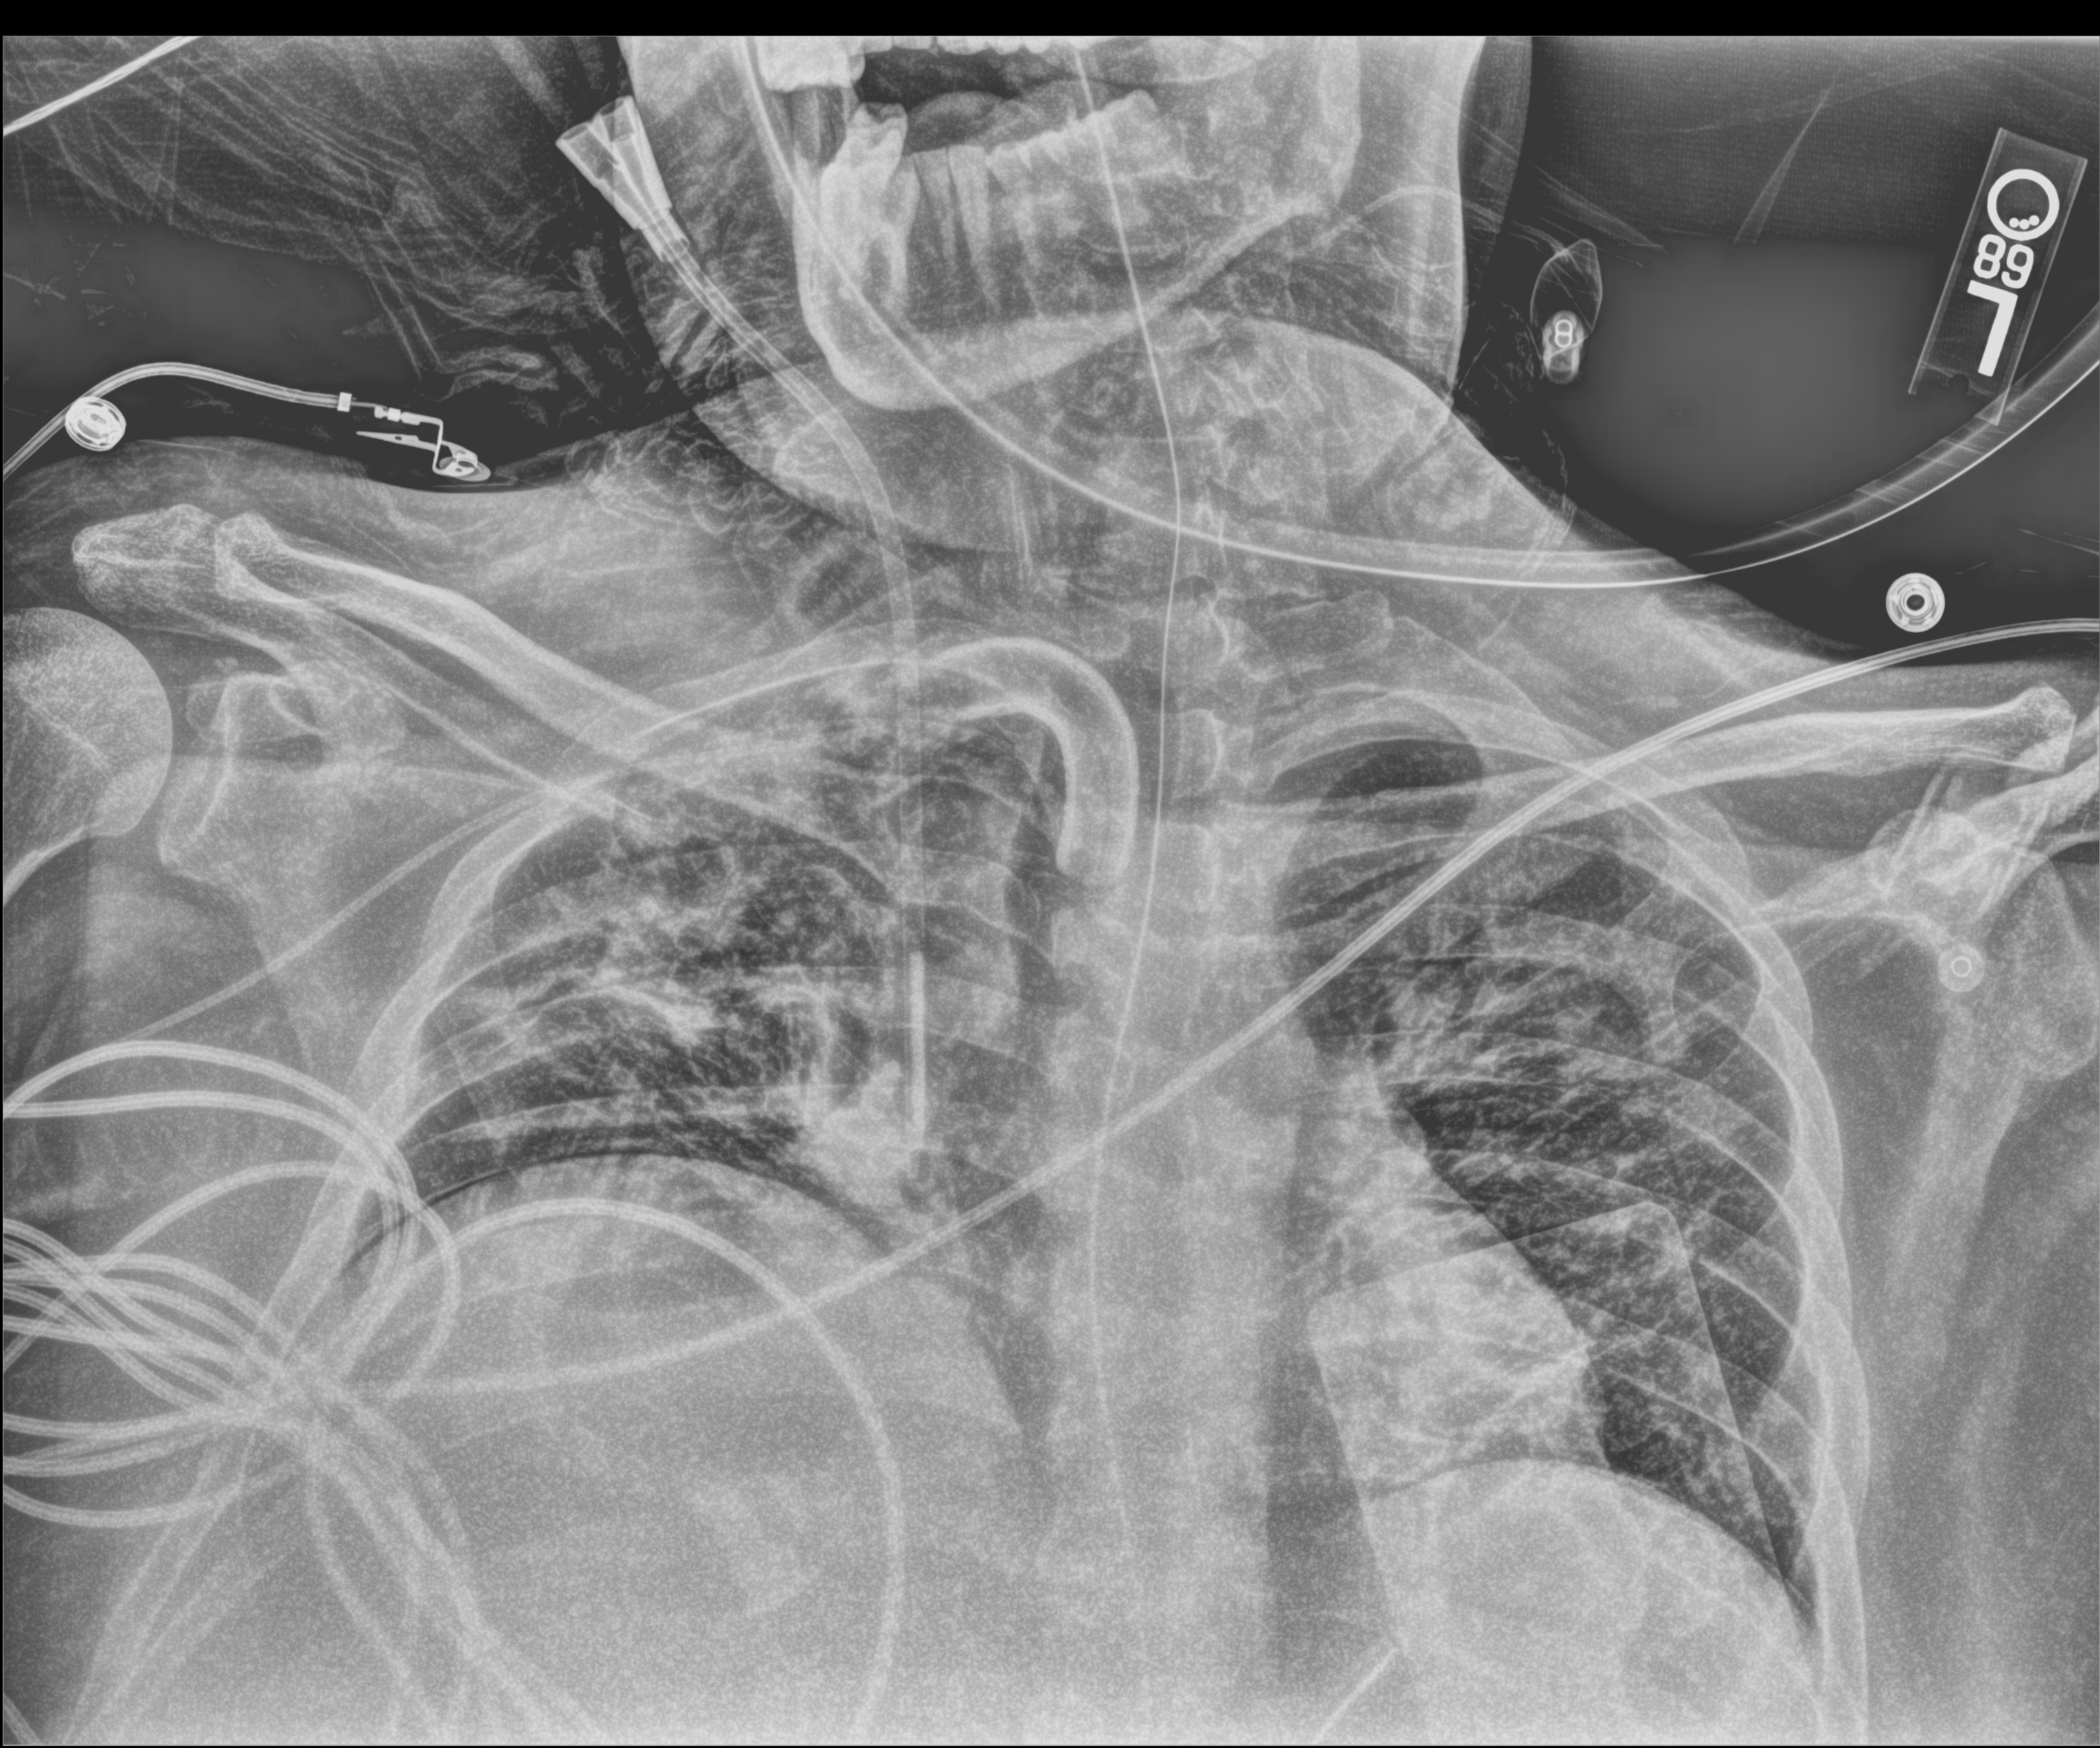
Bedside chest radiograph (computed radiography); anteroposterior (AP) projection. Adult patient hospitalised with COVID-19, age 18–59 years.
Hospital-stay facts (about this admission, not read from this image; timing relative to this image not recorded):
- admitted to intensive care during this hospital stay: yes
- length of hospital stay: 50 days